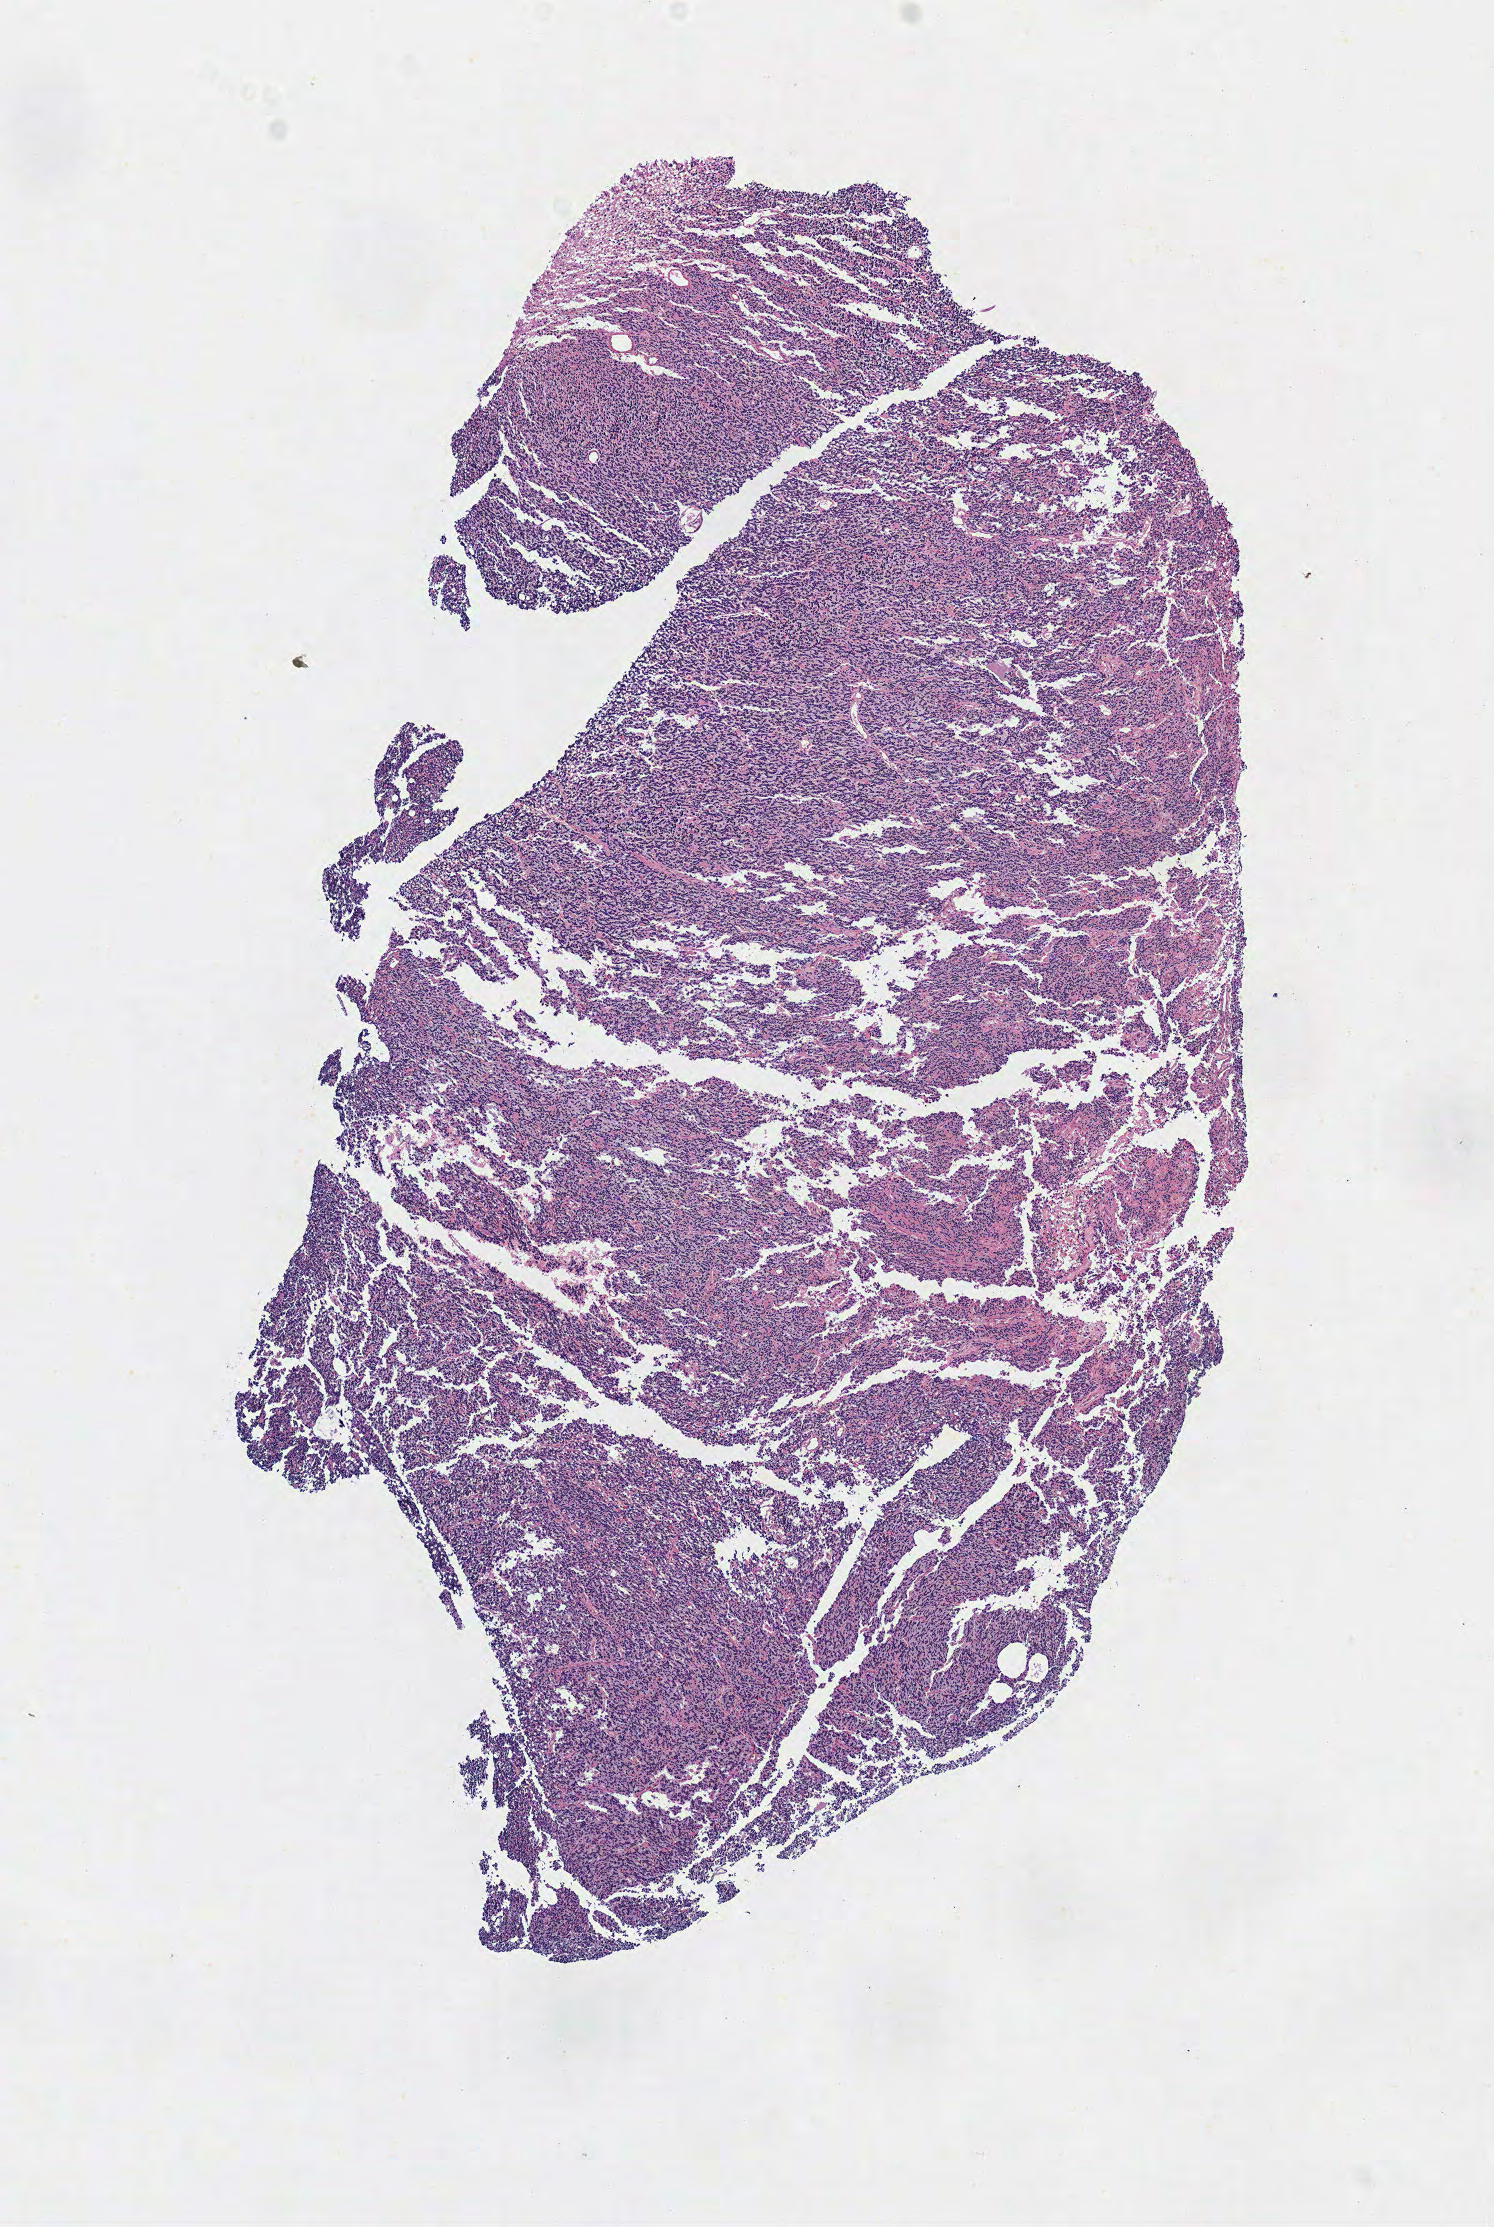
Digitized H&E tissue section (whole slide), shown as a low-resolution overview of the whole scanned area (about 5.9 x 8.8 mm), frozen section from the top of the tissue portion, sample: primary tumour, brain. Male, age 66 years at initial diagnosis. Histologic grade: G3 (poorly differentiated). Composition of this section per pathologist review: tumour cells 100%, tumour nuclei 85%, normal cells 0%, stromal cells 0%, necrosis 0%.
Laterality: left. Pathologic diagnosis: Oligodendroglioma, anaplastic.